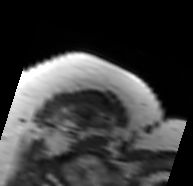
MRI of an extremity soft-tissue mass, one axial slice. Slice 64 of 91 in the series (ordered by position). MR volume resampled by the dataset authors to the PET/CT grid (not the native acquisition matrix). 3.27 mm slice thickness. 193 × 186 image matrix. Female patient. Case-level facts recorded for this patient, not image findings: histological type: malignant solitary fibrous tumor; grade: intermediate; site of the primary tumour: right thigh.
Structures marked on this image (expert contour drawn on MRI and transferred to this co-registered scan by the dataset authors):
- gross tumour volume including surrounding oedema: bounding box (x1, y1, x2, y2) in pixels: (47, 103, 116, 150)
- gross tumour volume (mass): (74, 108, 91, 129)